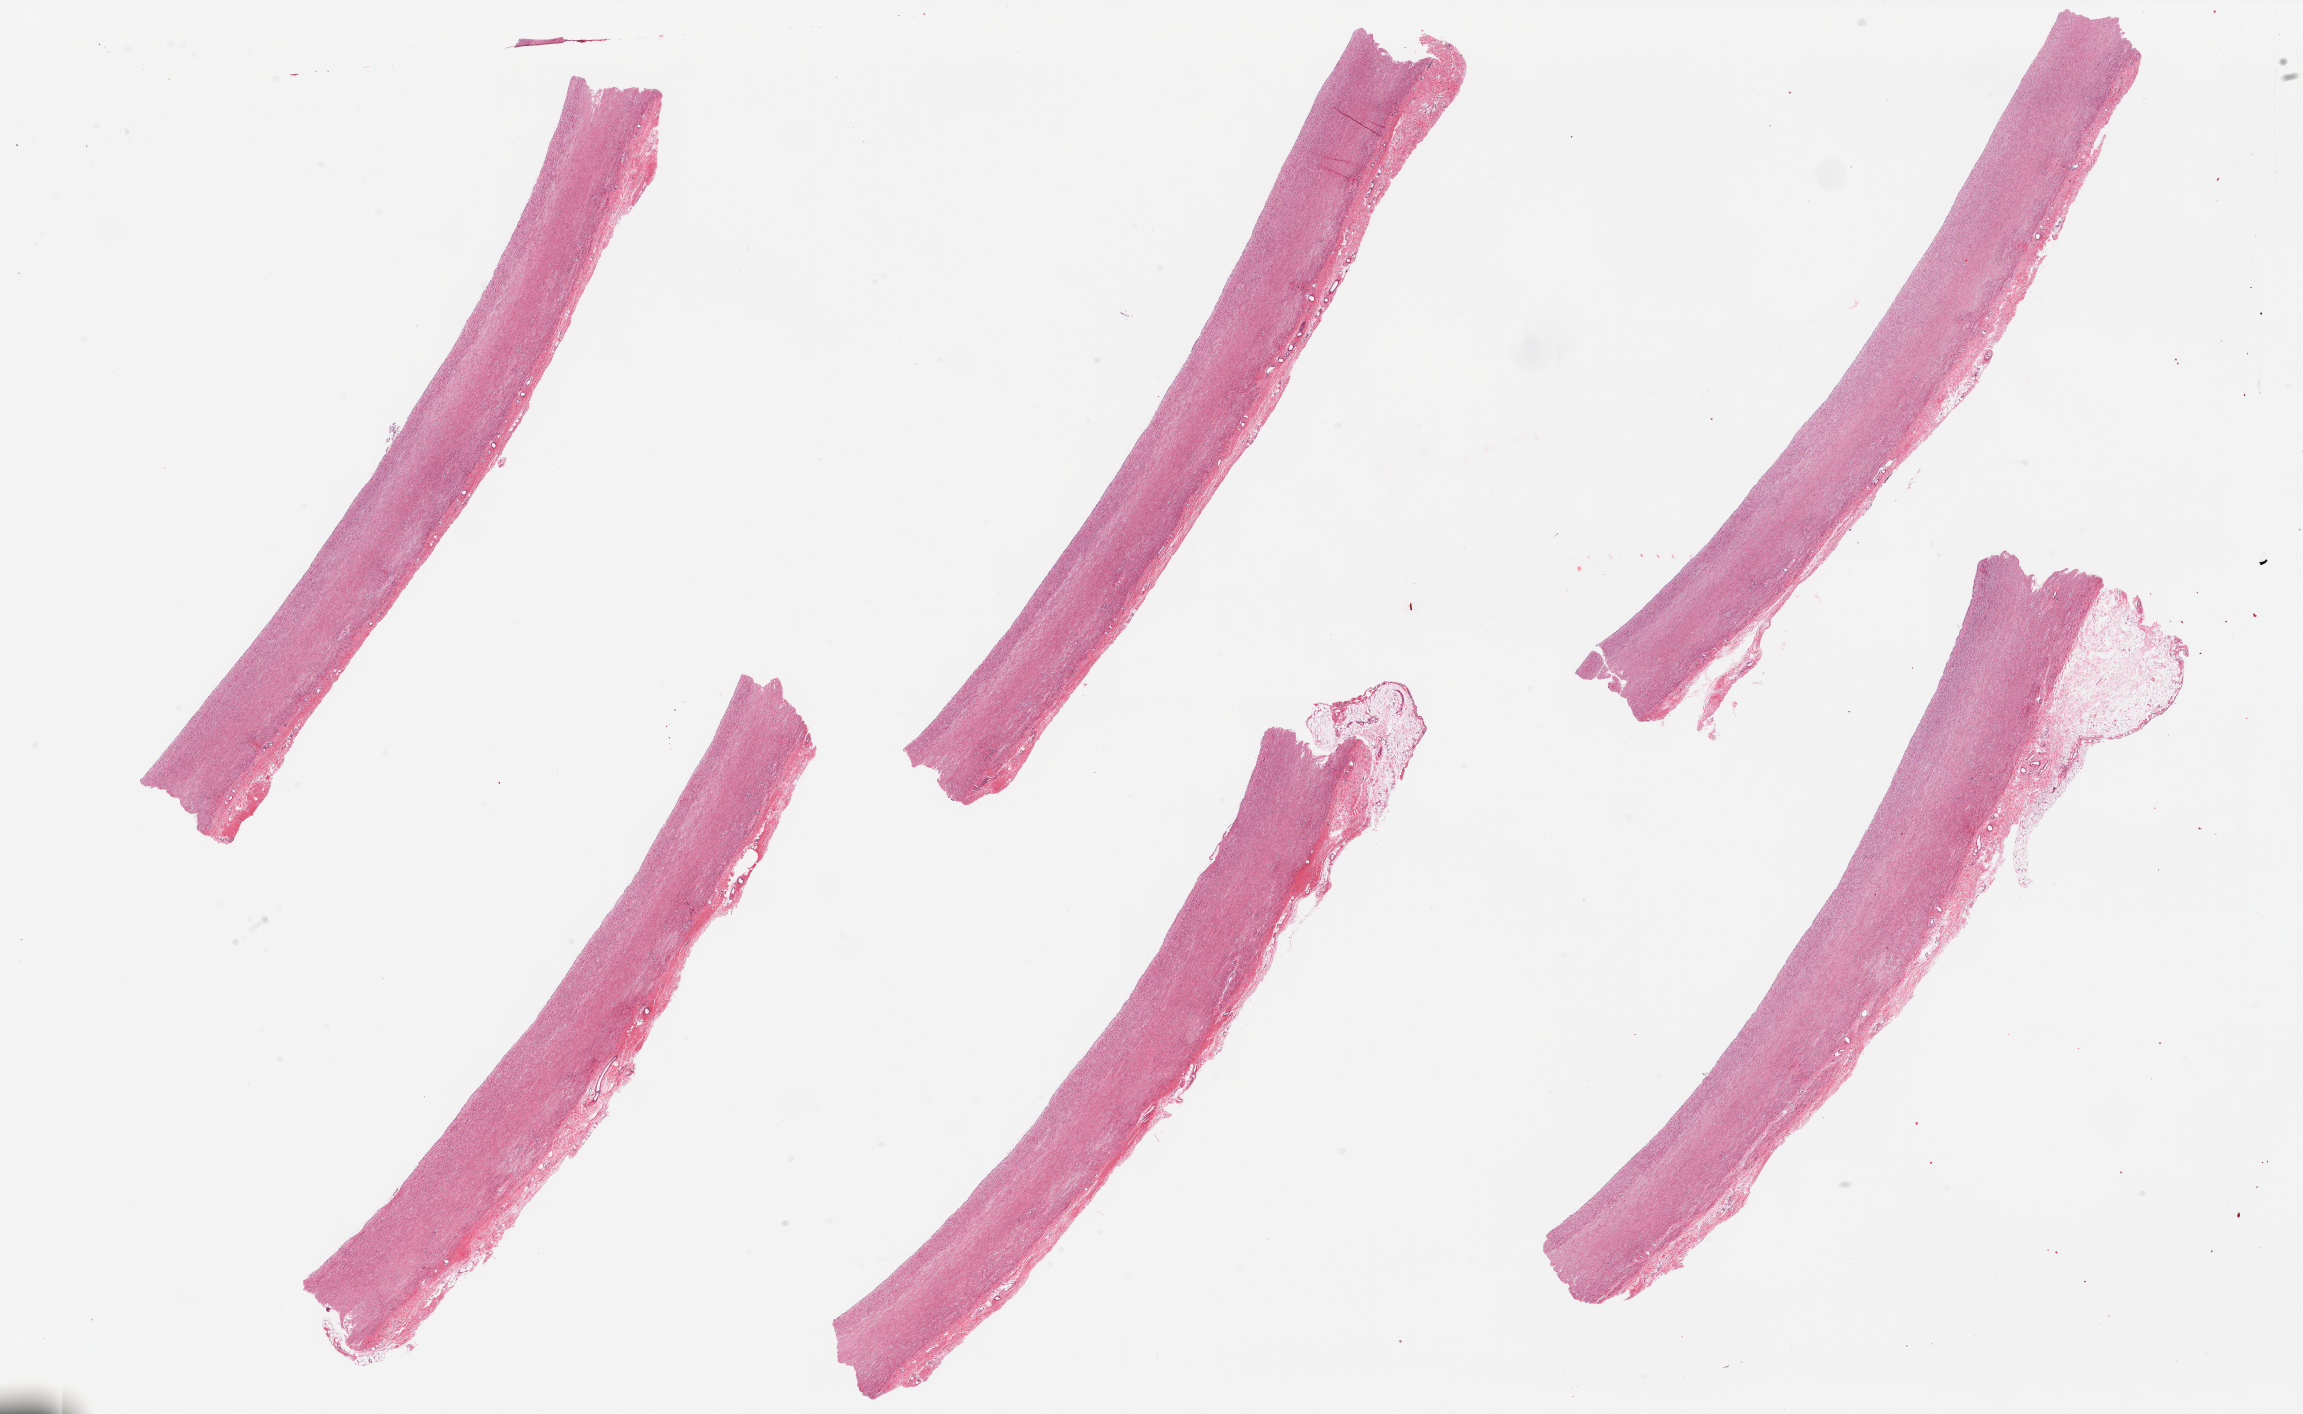
Hematoxylin and eosin (H&E) whole-slide image — a low-resolution overview of the entire scanned area, about 36.4 x 22.4 mm; PAXgene-fixed, paraffin-embedded tissue; section of aorta (target tissue); tissue donor sample. Donor sex: male.
* reviewer comment on this tissue sample: 6 pieces